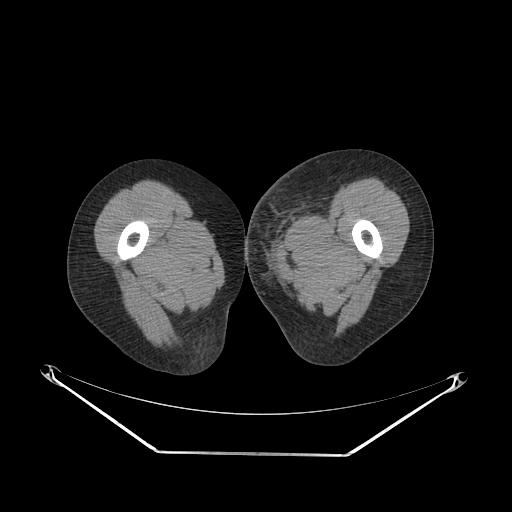
CT of an extremity soft-tissue mass (from a PET/CT study), one axial slice; position 42 of 267 along the scan axis; reconstruction kernel SOFT; 140 kVp; soft-tissue window (W 400 / L 40 HU); 3.75 mm slice thickness; 512 × 512 image matrix, field of view 500 × 500 mm. Female patient. Case-level facts recorded for this patient, not image findings: histological type: leiomyosarcoma; grade: high; site of the primary tumour: groin.
Annotated regions visible in this slice (expert contour drawn on MRI and transferred to this co-registered scan by the dataset authors):
- gross tumour volume including surrounding oedema: bounding box [x1, y1, x2, y2] px = [244, 185, 327, 255]